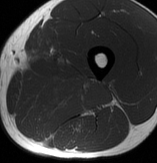
MRI of an extremity soft-tissue mass, one axial slice; position 34 of 70 along the scan axis; MR volume resampled by the dataset authors to the PET/CT grid (not the native acquisition matrix); 3.27 mm slice thickness; 157 × 163 image matrix. Male patient. From the clinical record (not read from this slice): histological type: extraskeletal osteosarcoma; grade: high; site of the primary tumour: left adductur.
Annotated regions visible in this slice (expert contour drawn on MRI and transferred to this co-registered scan by the dataset authors):
- gross tumour volume (mass): box from (x=13, y=69) to (x=114, y=137) px